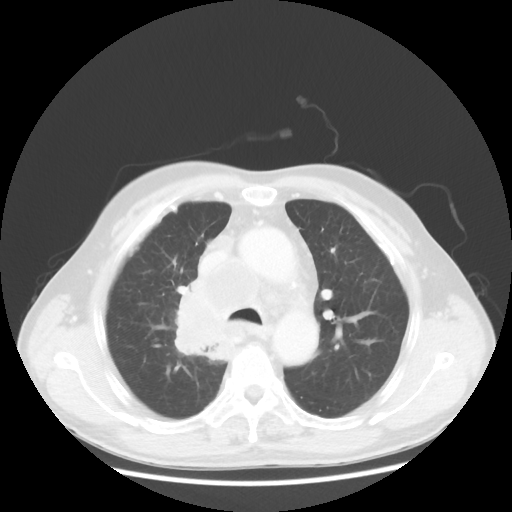
Chest CT, one axial slice. Position 84 of 124 along the scan axis. Lung window (W 1500 / L -600 HU). 5 mm slice thickness. 512 × 512 image matrix, field of view 382 × 382 mm. Patient: male, 64 years. From the clinical record (not read from this slice): clinical TNM (as recorded): T3 N3 M0.
Outlined on this slice (rectangle marked by the reading radiologist):
- lung tumour (recorded histology: small cell carcinoma): bounding box [x1, y1, x2, y2] px = [168, 280, 233, 365]